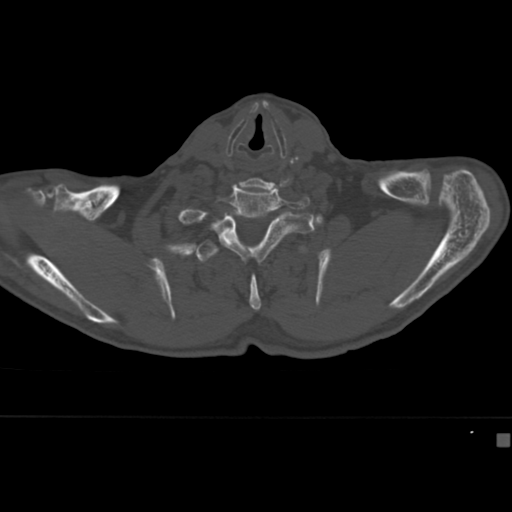
CT including the spine, one axial slice; position 352 of 430 along the scan axis; reconstruction kernel Br40s; bone window (W 1800 / L 400 HU); 512 × 512 image matrix. Male patient, age 64 years. From the clinical record (not read from this slice): primary cancer: uterus; vertebrae with lytic lesions (as recorded): T1, T4, T5, T7, L5.
Structures marked on this image (semi-automatically segmented with operator editing):
- T2 vertebra: box from (x=195, y=240) to (x=308, y=311) px